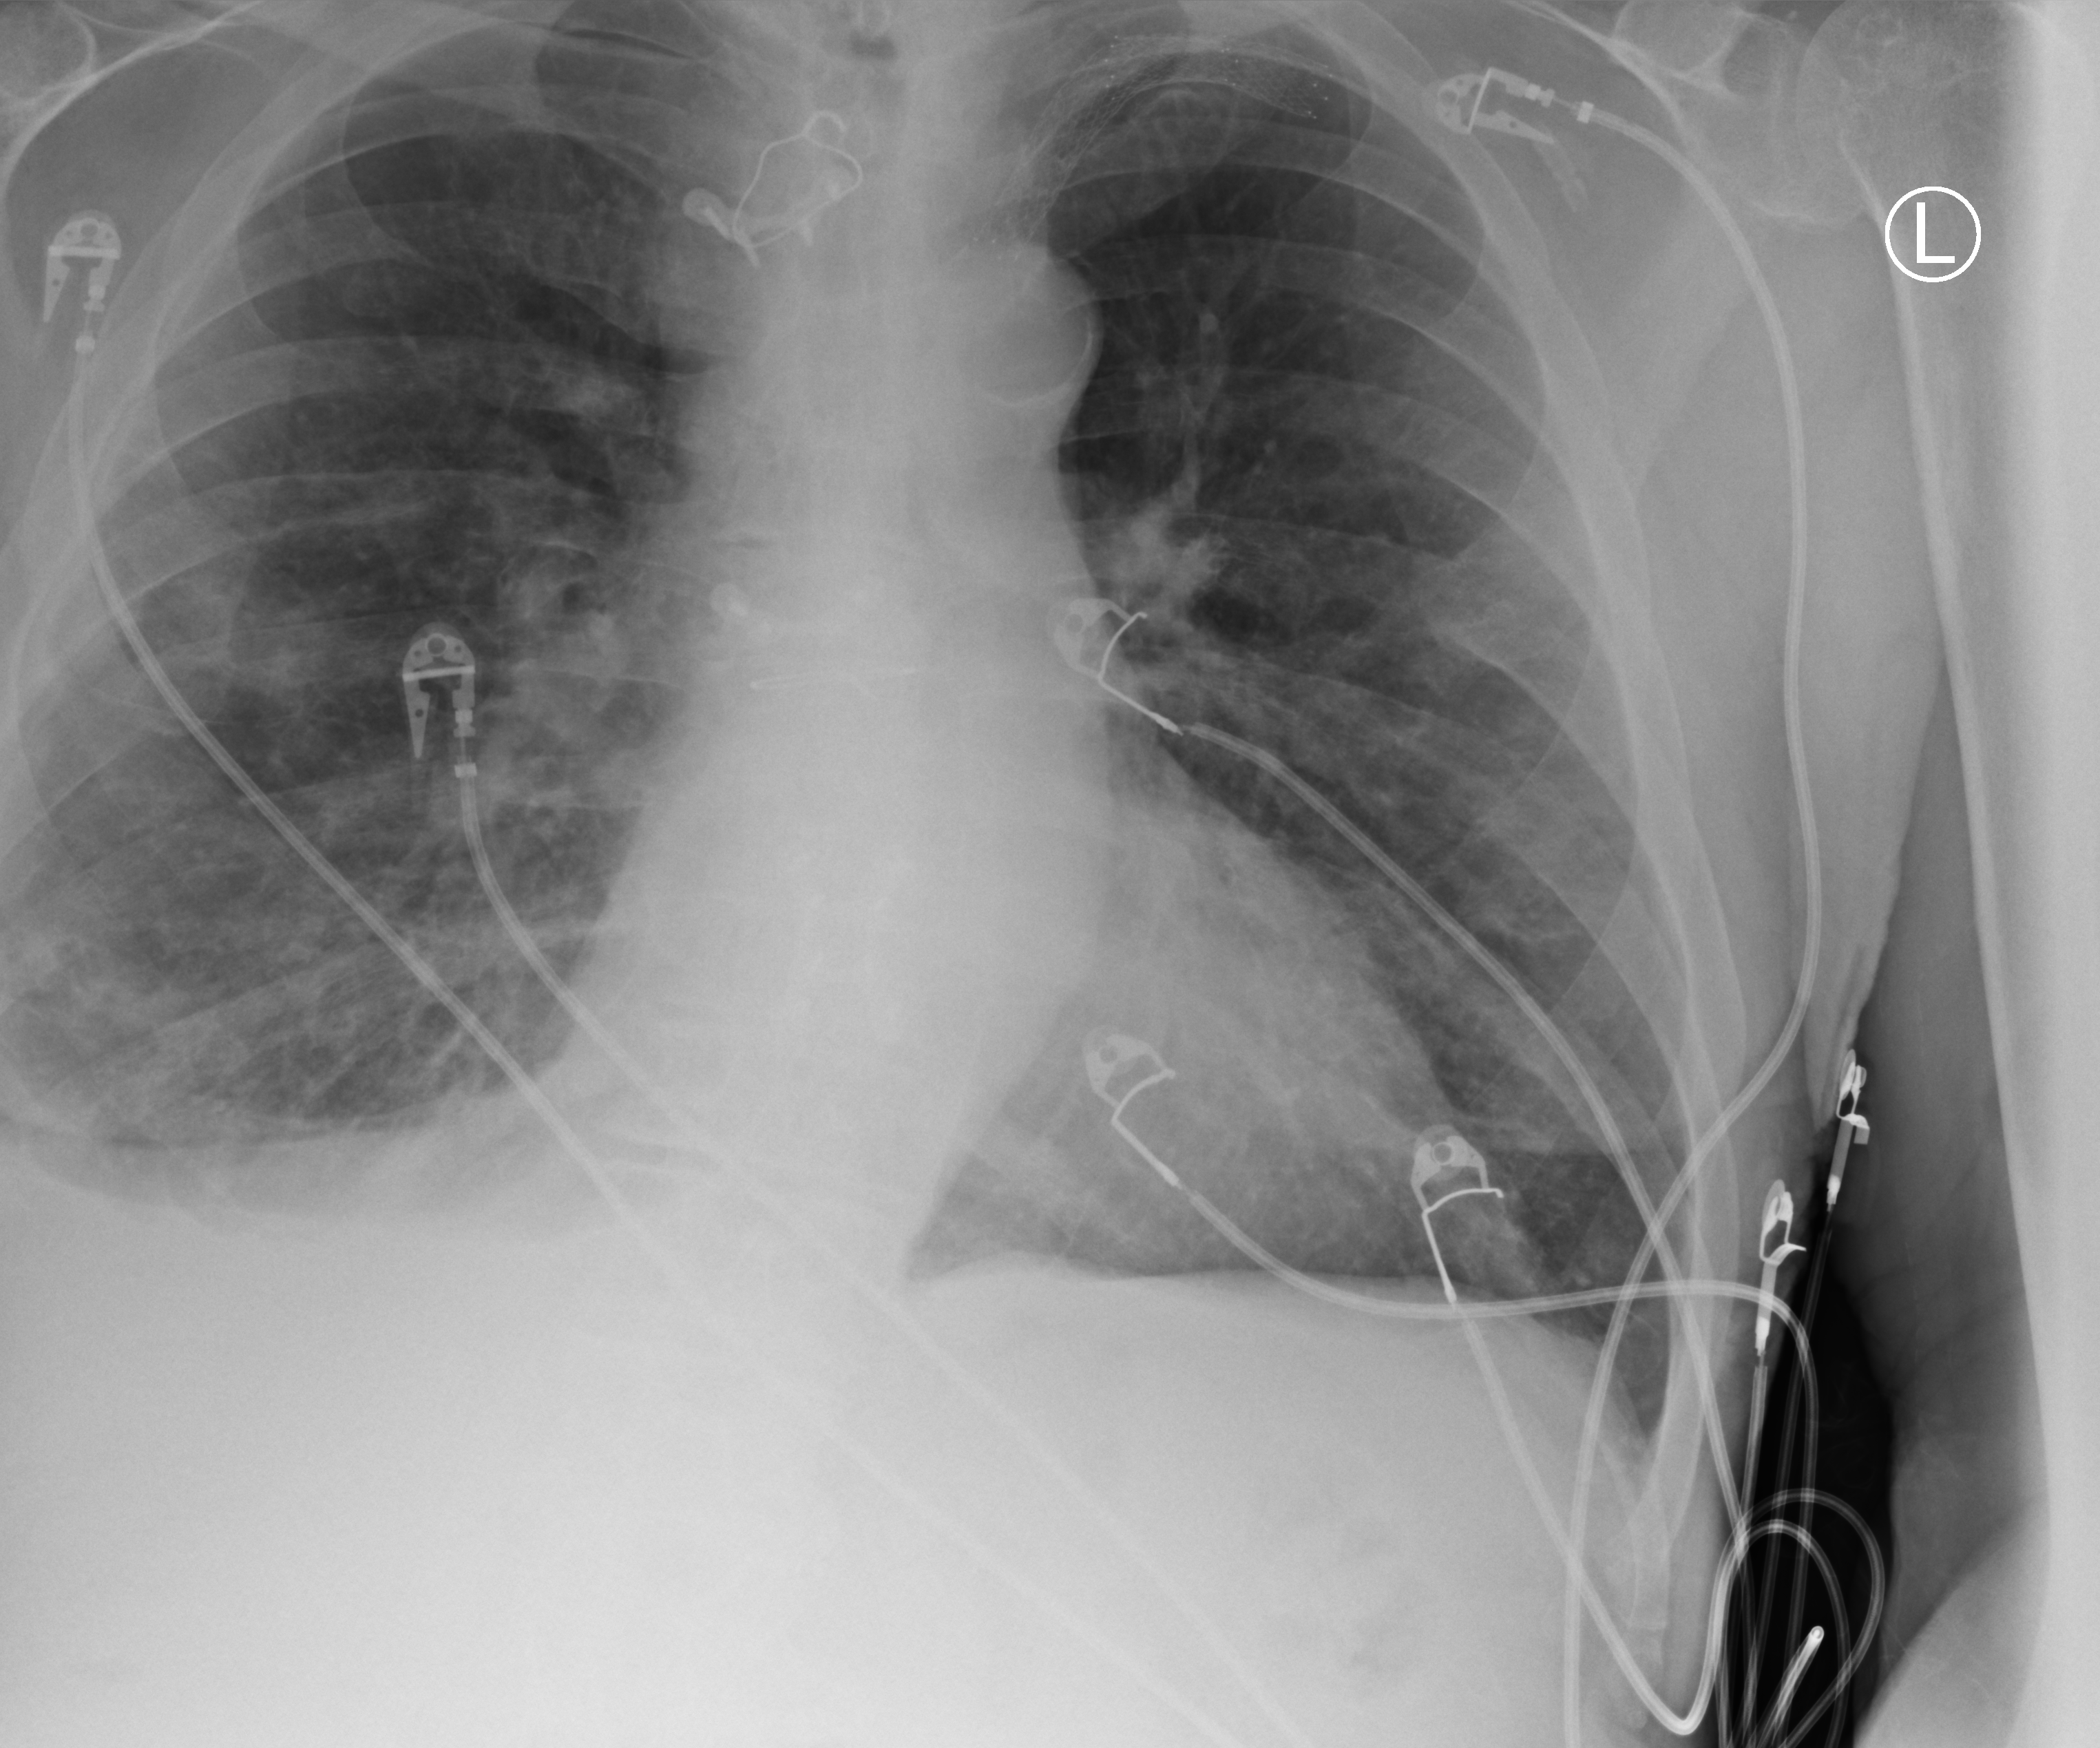
Portable chest radiograph, anteroposterior (AP) projection. Patient hospitalised with COVID-19; male, aged 75–90 years.
Admission-level facts for this patient (not findings on this image; timing relative to this image not recorded): admitted to intensive care during this hospital stay: no; mechanically ventilated during this hospital stay: no.